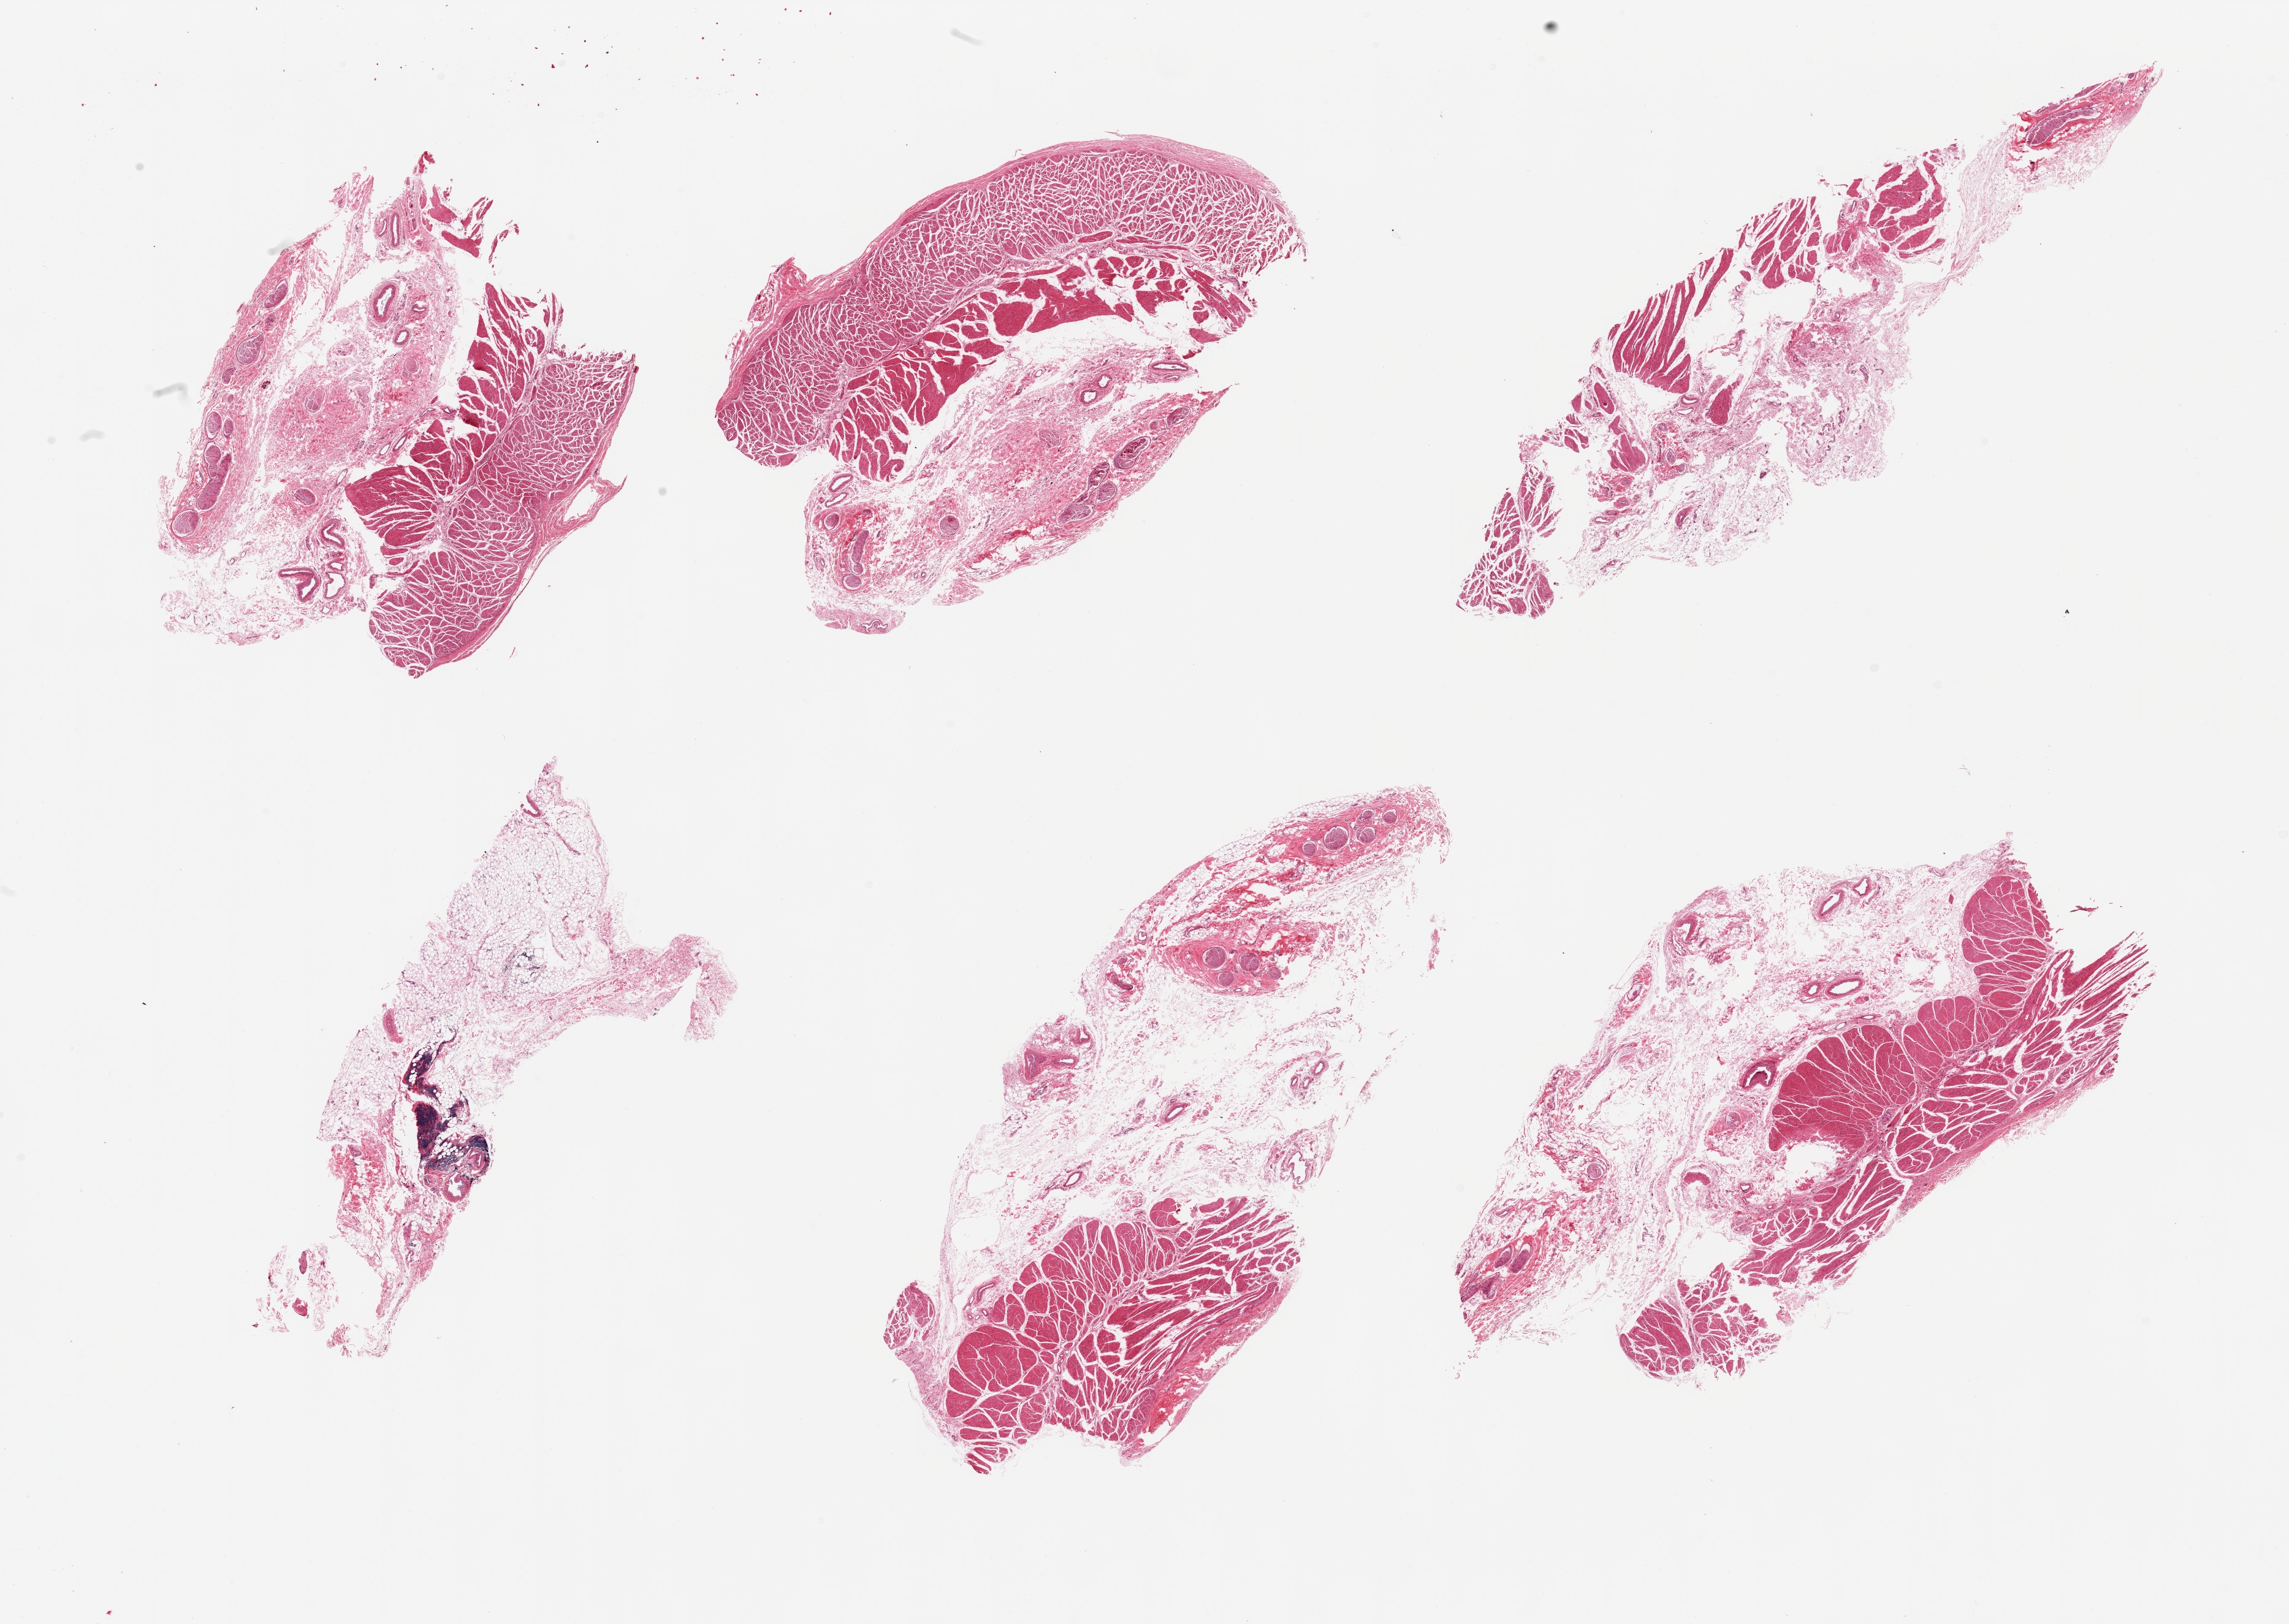
Hematoxylin and eosin (H&E) whole-slide image, brightfield — a low-resolution overview of the entire scanned area, about 29.5 x 21.0 mm (from a 20x scan); PAXgene-fixed paraffin-embedded (PFPE) section; sampled site (target tissue): esophageal muscle; donor tissue sample.
• review note (as recorded): 6 pieces; 5 of 6 include muscularis, but ~50% of each is residual fat, vessels and significant component of nerve, one piece is entirely fat/incidental lymph node/vessels